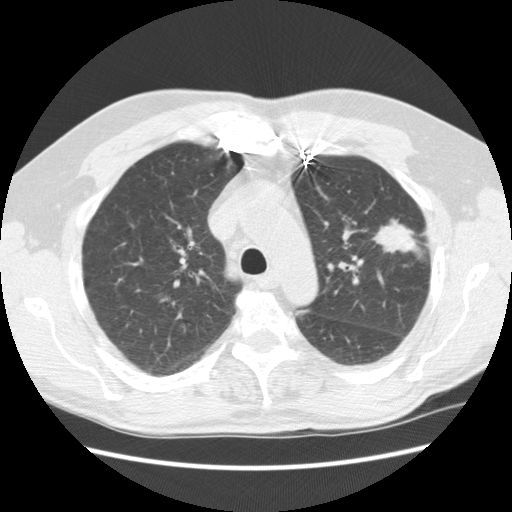
Low-dose screening chest CT, one axial slice; reconstruction kernel STANDARD; lung window (W 1500 / L -600 HU); 2.5 mm slice thickness; 512 × 512 image matrix, field of view 362 × 362 mm.
Outlined on this slice (manually delineated by an expert):
- lesion 1 (tumor, upper lobe of left lung): bounding box <374,219,419,253> (left, top, right, bottom; pixels)